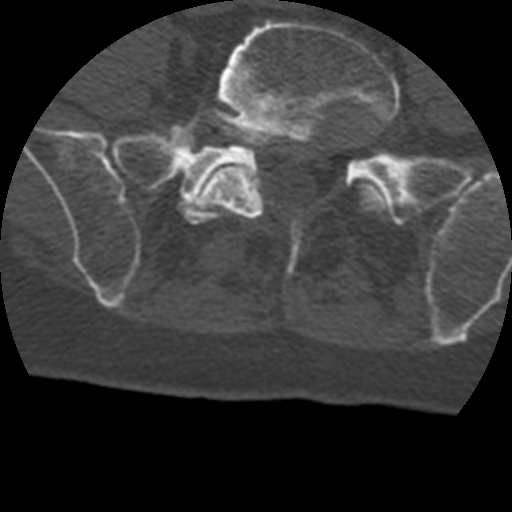
CT including the spine, one axial slice. Slice 35 of 399 in the series (ordered by position). 120 kVp. Bone window (W 1800 / L 400 HU). 1.25 mm slice thickness. 512 × 512 image matrix, field of view 160 × 160 mm. Patient age 69 years. From the clinical record (not read from this slice): primary cancer: prostate.
Annotated regions visible in this slice (semi-automatically segmented with operator editing):
- L5 vertebra: bounding box [x1, y1, x2, y2] px = [168, 20, 400, 276]